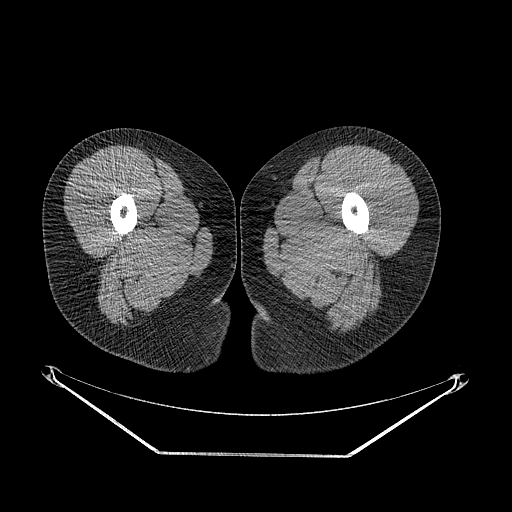
CT of an extremity soft-tissue mass (from a PET/CT study), one axial slice; reconstruction kernel STANDARD; 120 kVp; soft-tissue window (W 400 / L 40 HU); 3.75 mm slice thickness; 512 × 512 image matrix, field of view 500 × 500 mm. Female patient. From the clinical record (not read from this slice): histological type: epithelioid sarcoma; grade: intermediate; site of the primary tumour: right buttock.
Annotated regions visible in this slice (expert contour drawn on MRI and transferred to this co-registered scan by the dataset authors):
- gross tumour volume including surrounding oedema: bounding box (x1, y1, x2, y2) in pixels: (187, 327, 225, 373)